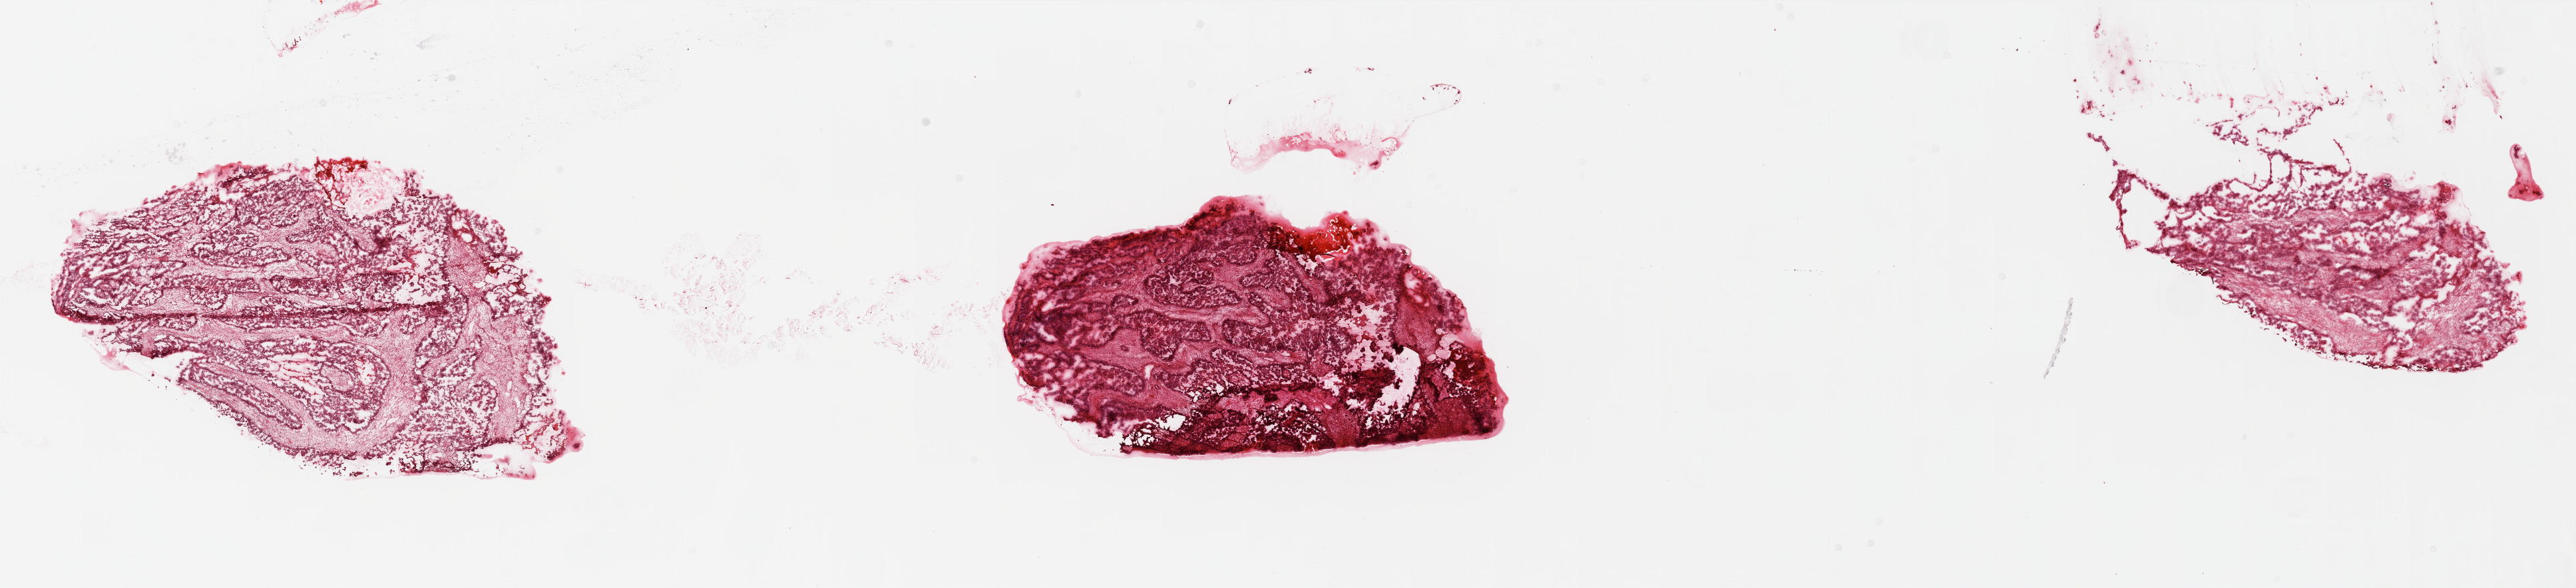
H&E-stained whole-slide image — a low-resolution overview of the entire scanned area, about 31.0 x 7.1 mm (acquisition: 20x scan). Frozen section from the top of the tissue portion. Sample: primary tumour, ovary. Female, age 53 years at initial diagnosis. Histologic grade: G3 (poorly differentiated). Pathologist review of this section (percent, as recorded): tumour cells 75%, tumour nuclei 85%, normal cells 0%, stromal cells 25%, necrosis 0%.
* FIGO stage: IV
* pathologic diagnosis: Serous cystadenocarcinoma, NOS